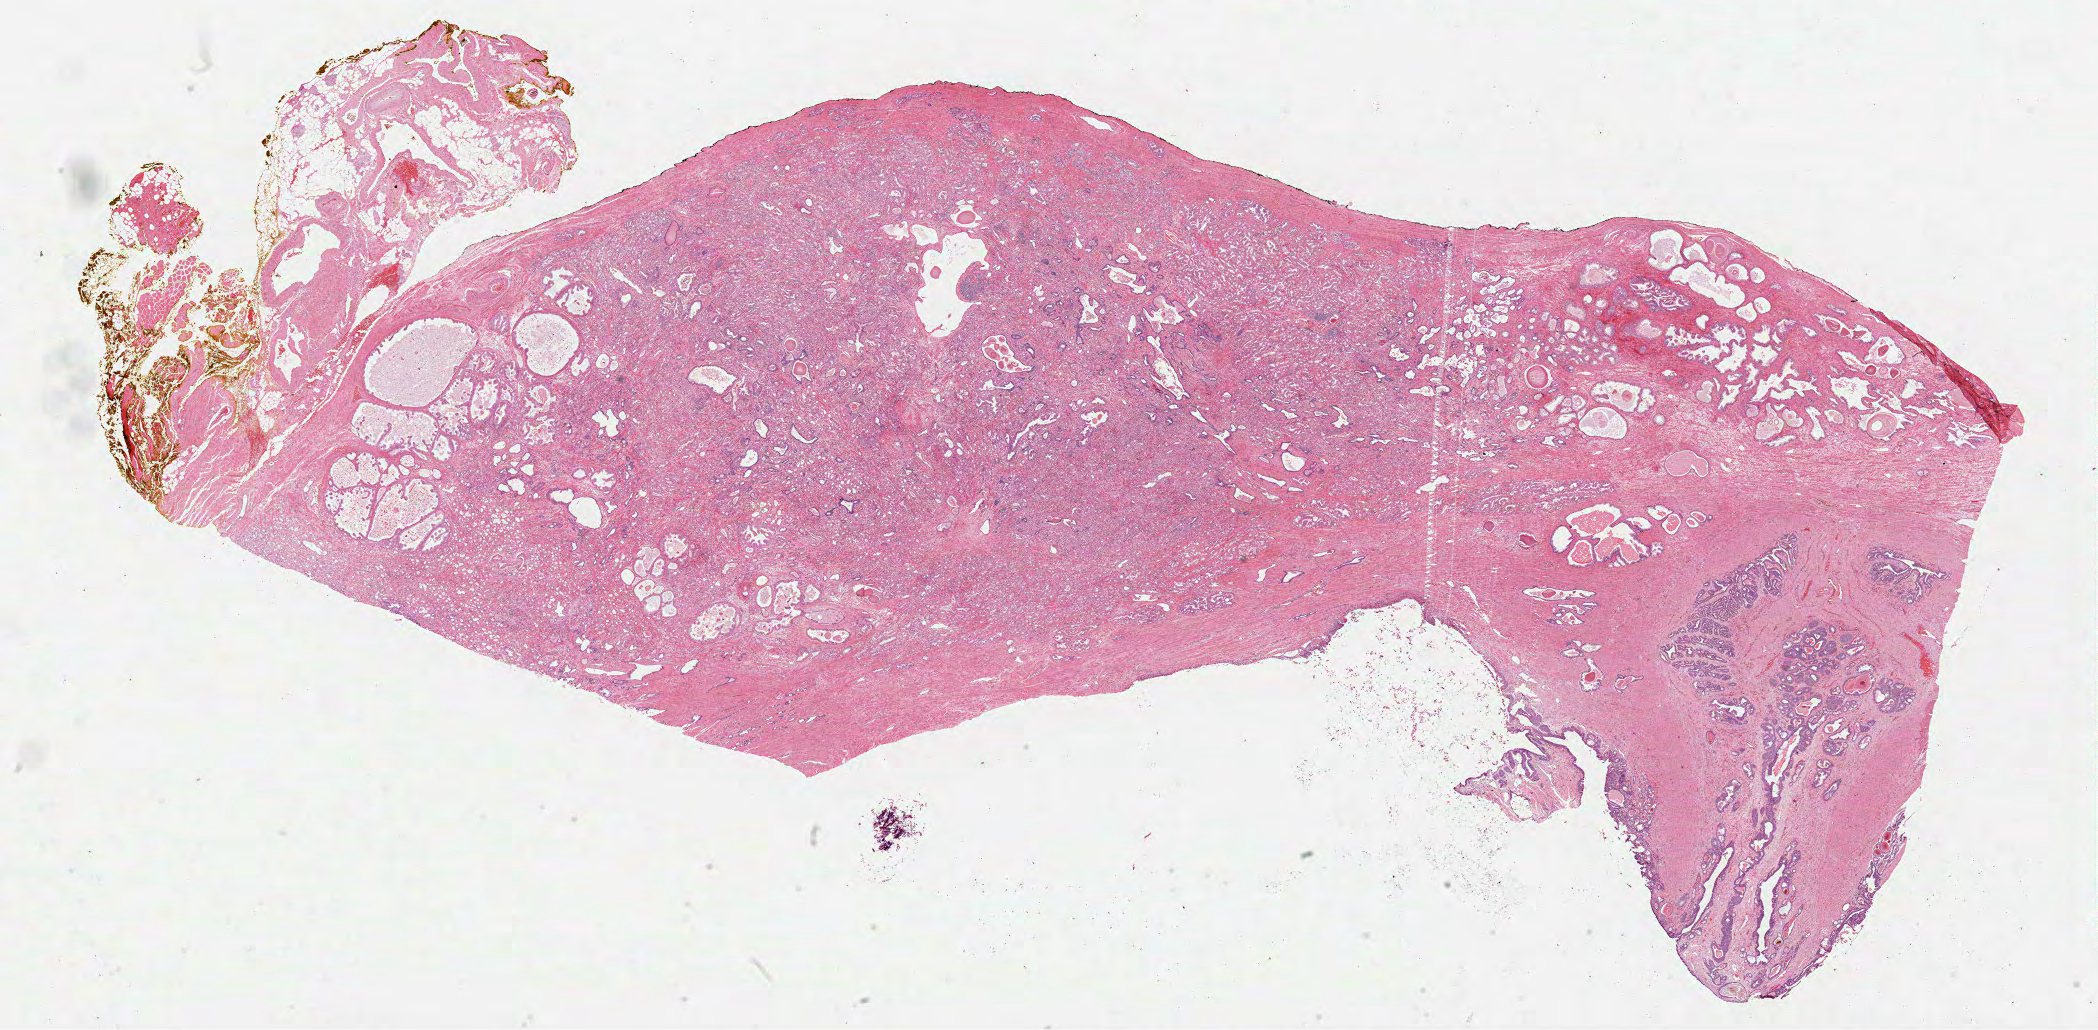
H&E-stained whole-slide image — shown as a low-resolution overview of the whole scanned area (about 33.8 x 16.6 mm, slide scanned at 40x). Formalin-fixed paraffin-embedded (FFPE) diagnostic section. Sample: primary tumour, prostate. Male, age 61 years at initial diagnosis. Gleason score: 7 (4+3).
* laterality: left
* pathologic diagnosis: Acinar cell carcinoma